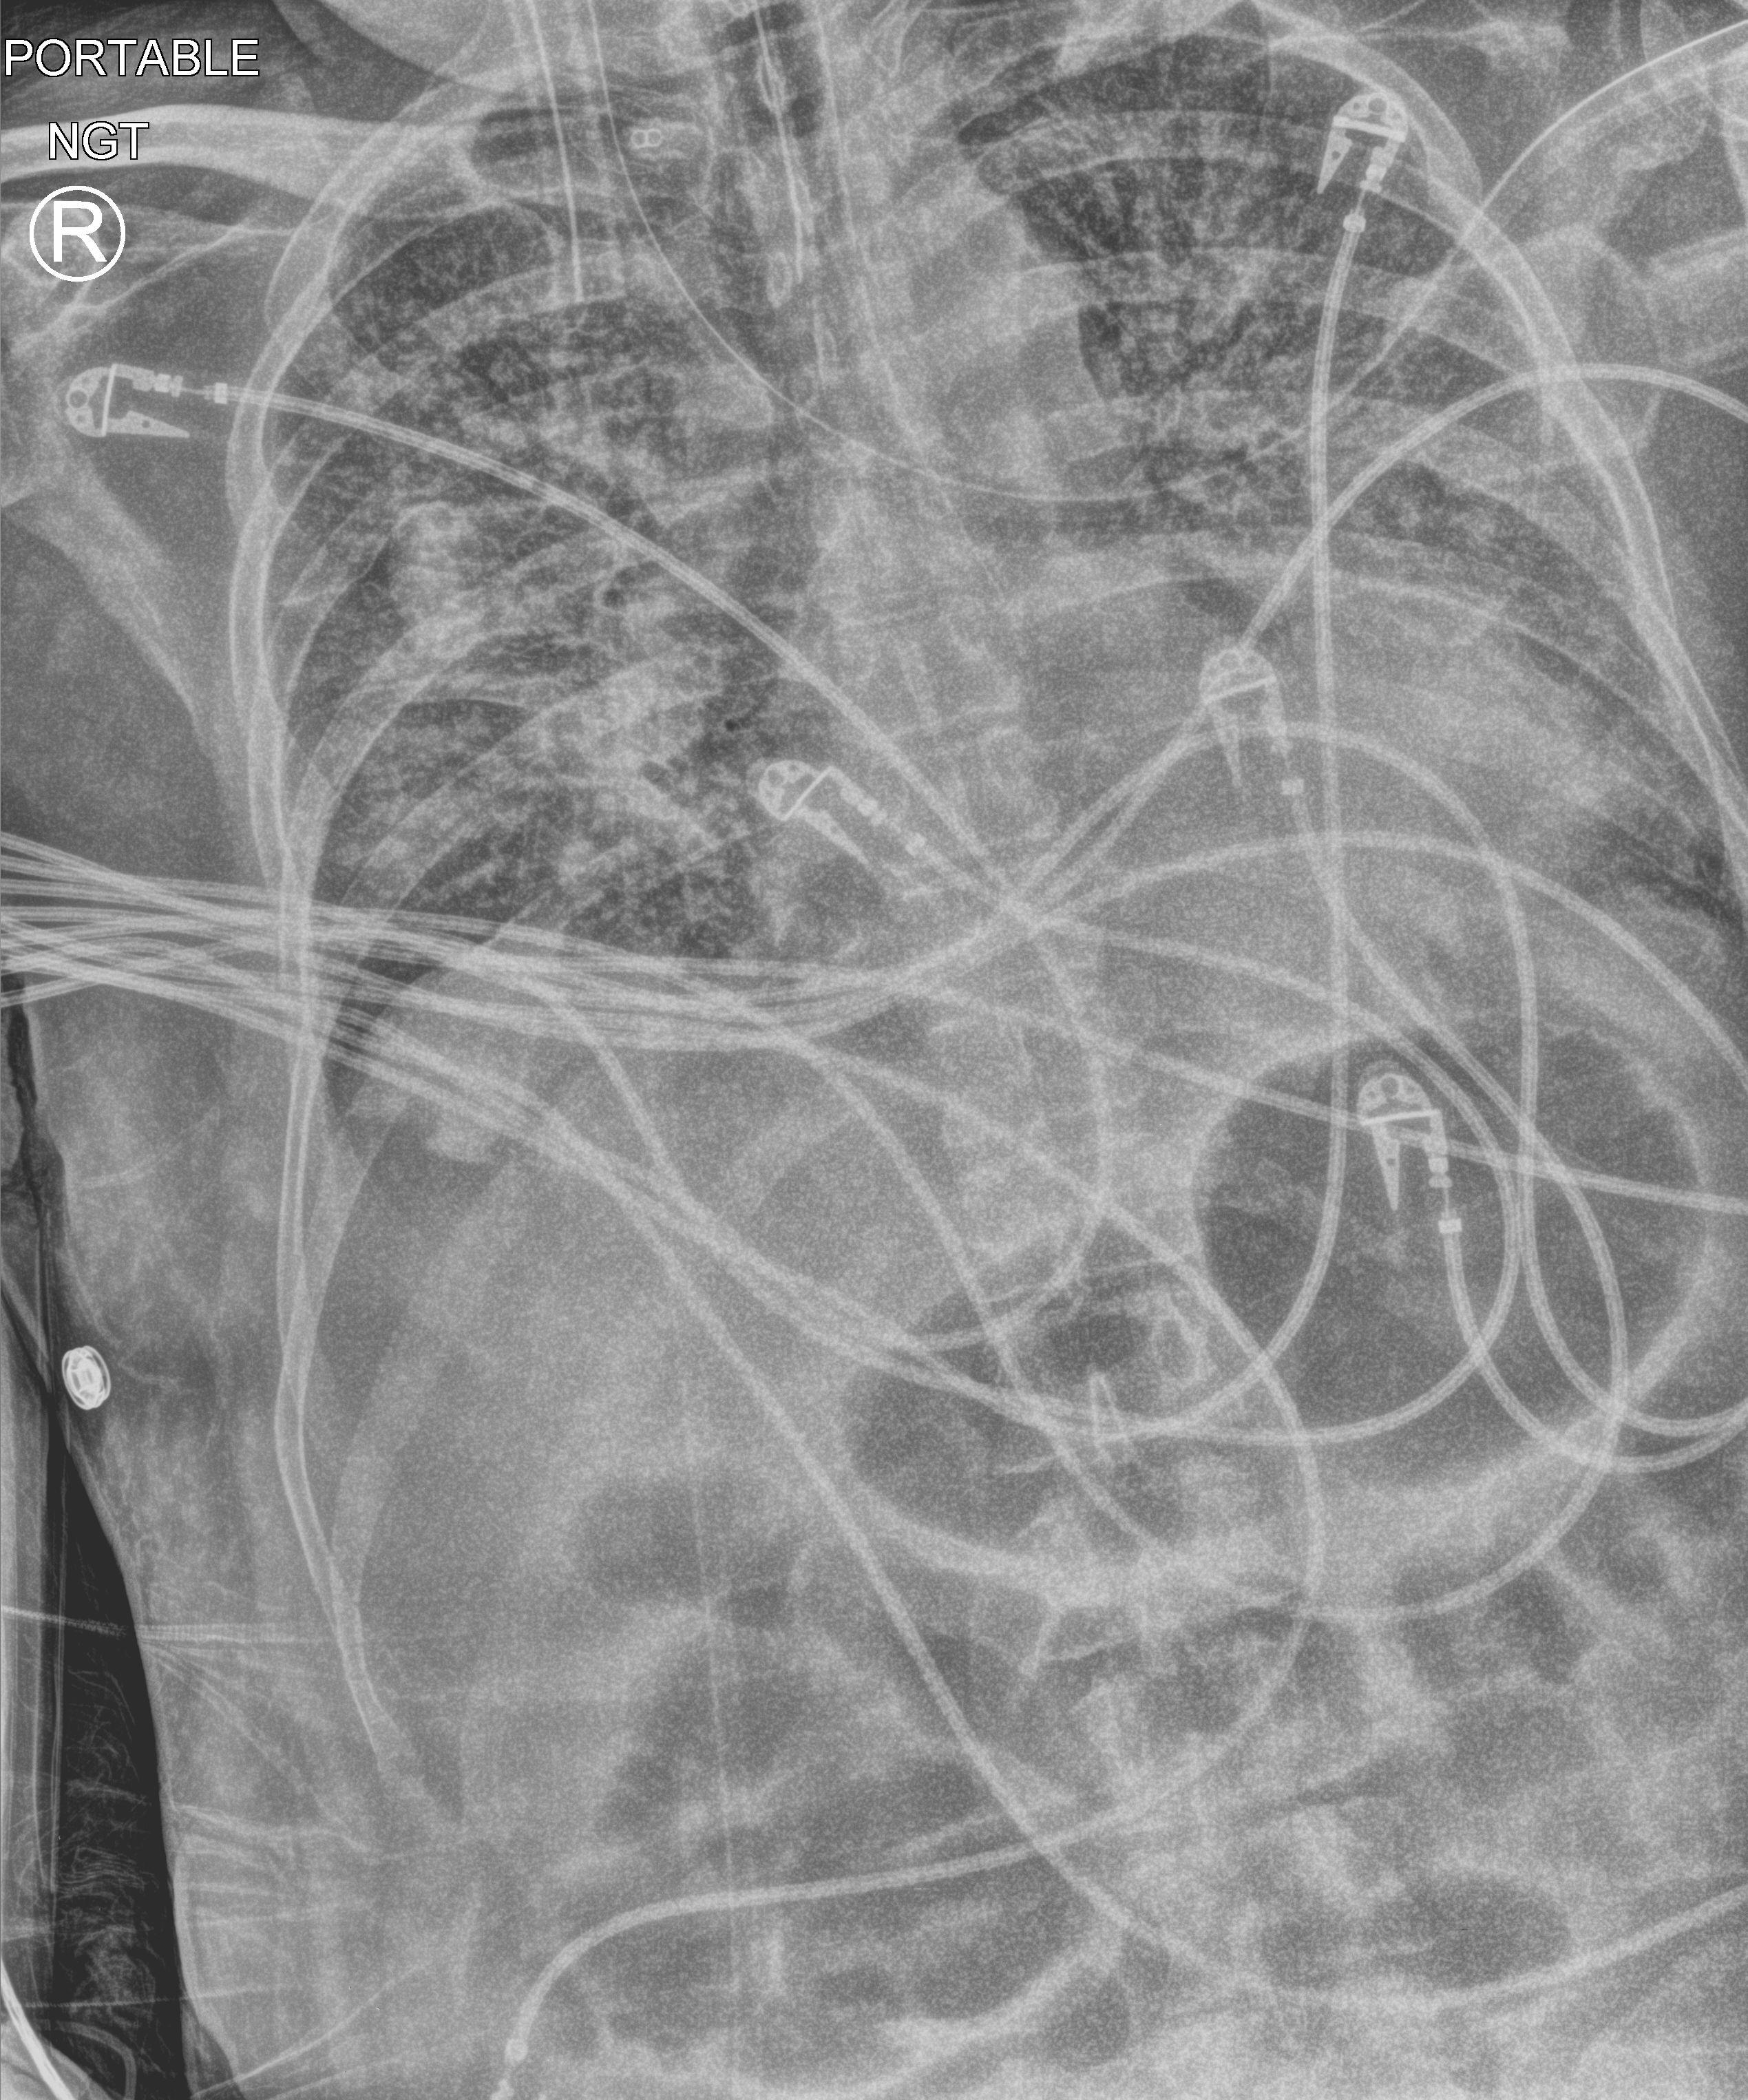
Portable chest radiograph; anteroposterior (AP) projection. Male patient hospitalised with COVID-19, age 60–74 years.
From the hospital-stay record, not from the radiograph (when in the stay this image was taken is not recorded): hypertension (admission record): yes; other chronic lung disease (admission record): no.